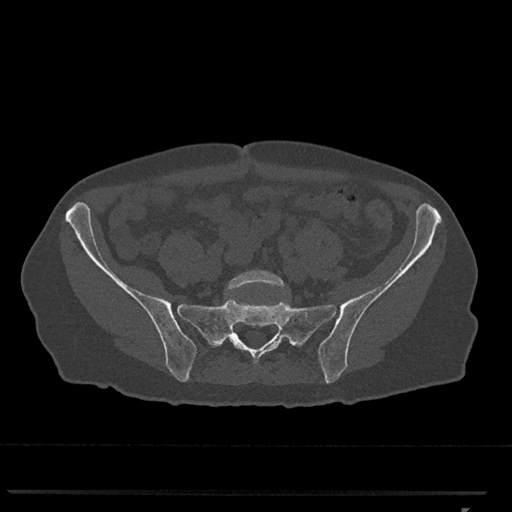
CT including the spine, one axial slice. Position 110 of 793 along the scan axis. Reconstruction kernel Br40s/3. 120 kVp. Bone window (W 1800 / L 400 HU). 0.5 mm slice thickness. 512 × 512 image matrix, field of view 380 × 380 mm. Female patient, age 62 years. Case-level facts recorded for this patient, not image findings: primary cancer: renal.
Outlined on this slice (semi-automatic segmentation, software-assisted and operator-edited):
- L5 vertebra: bounding box [x1, y1, x2, y2] px = [227, 270, 285, 290]